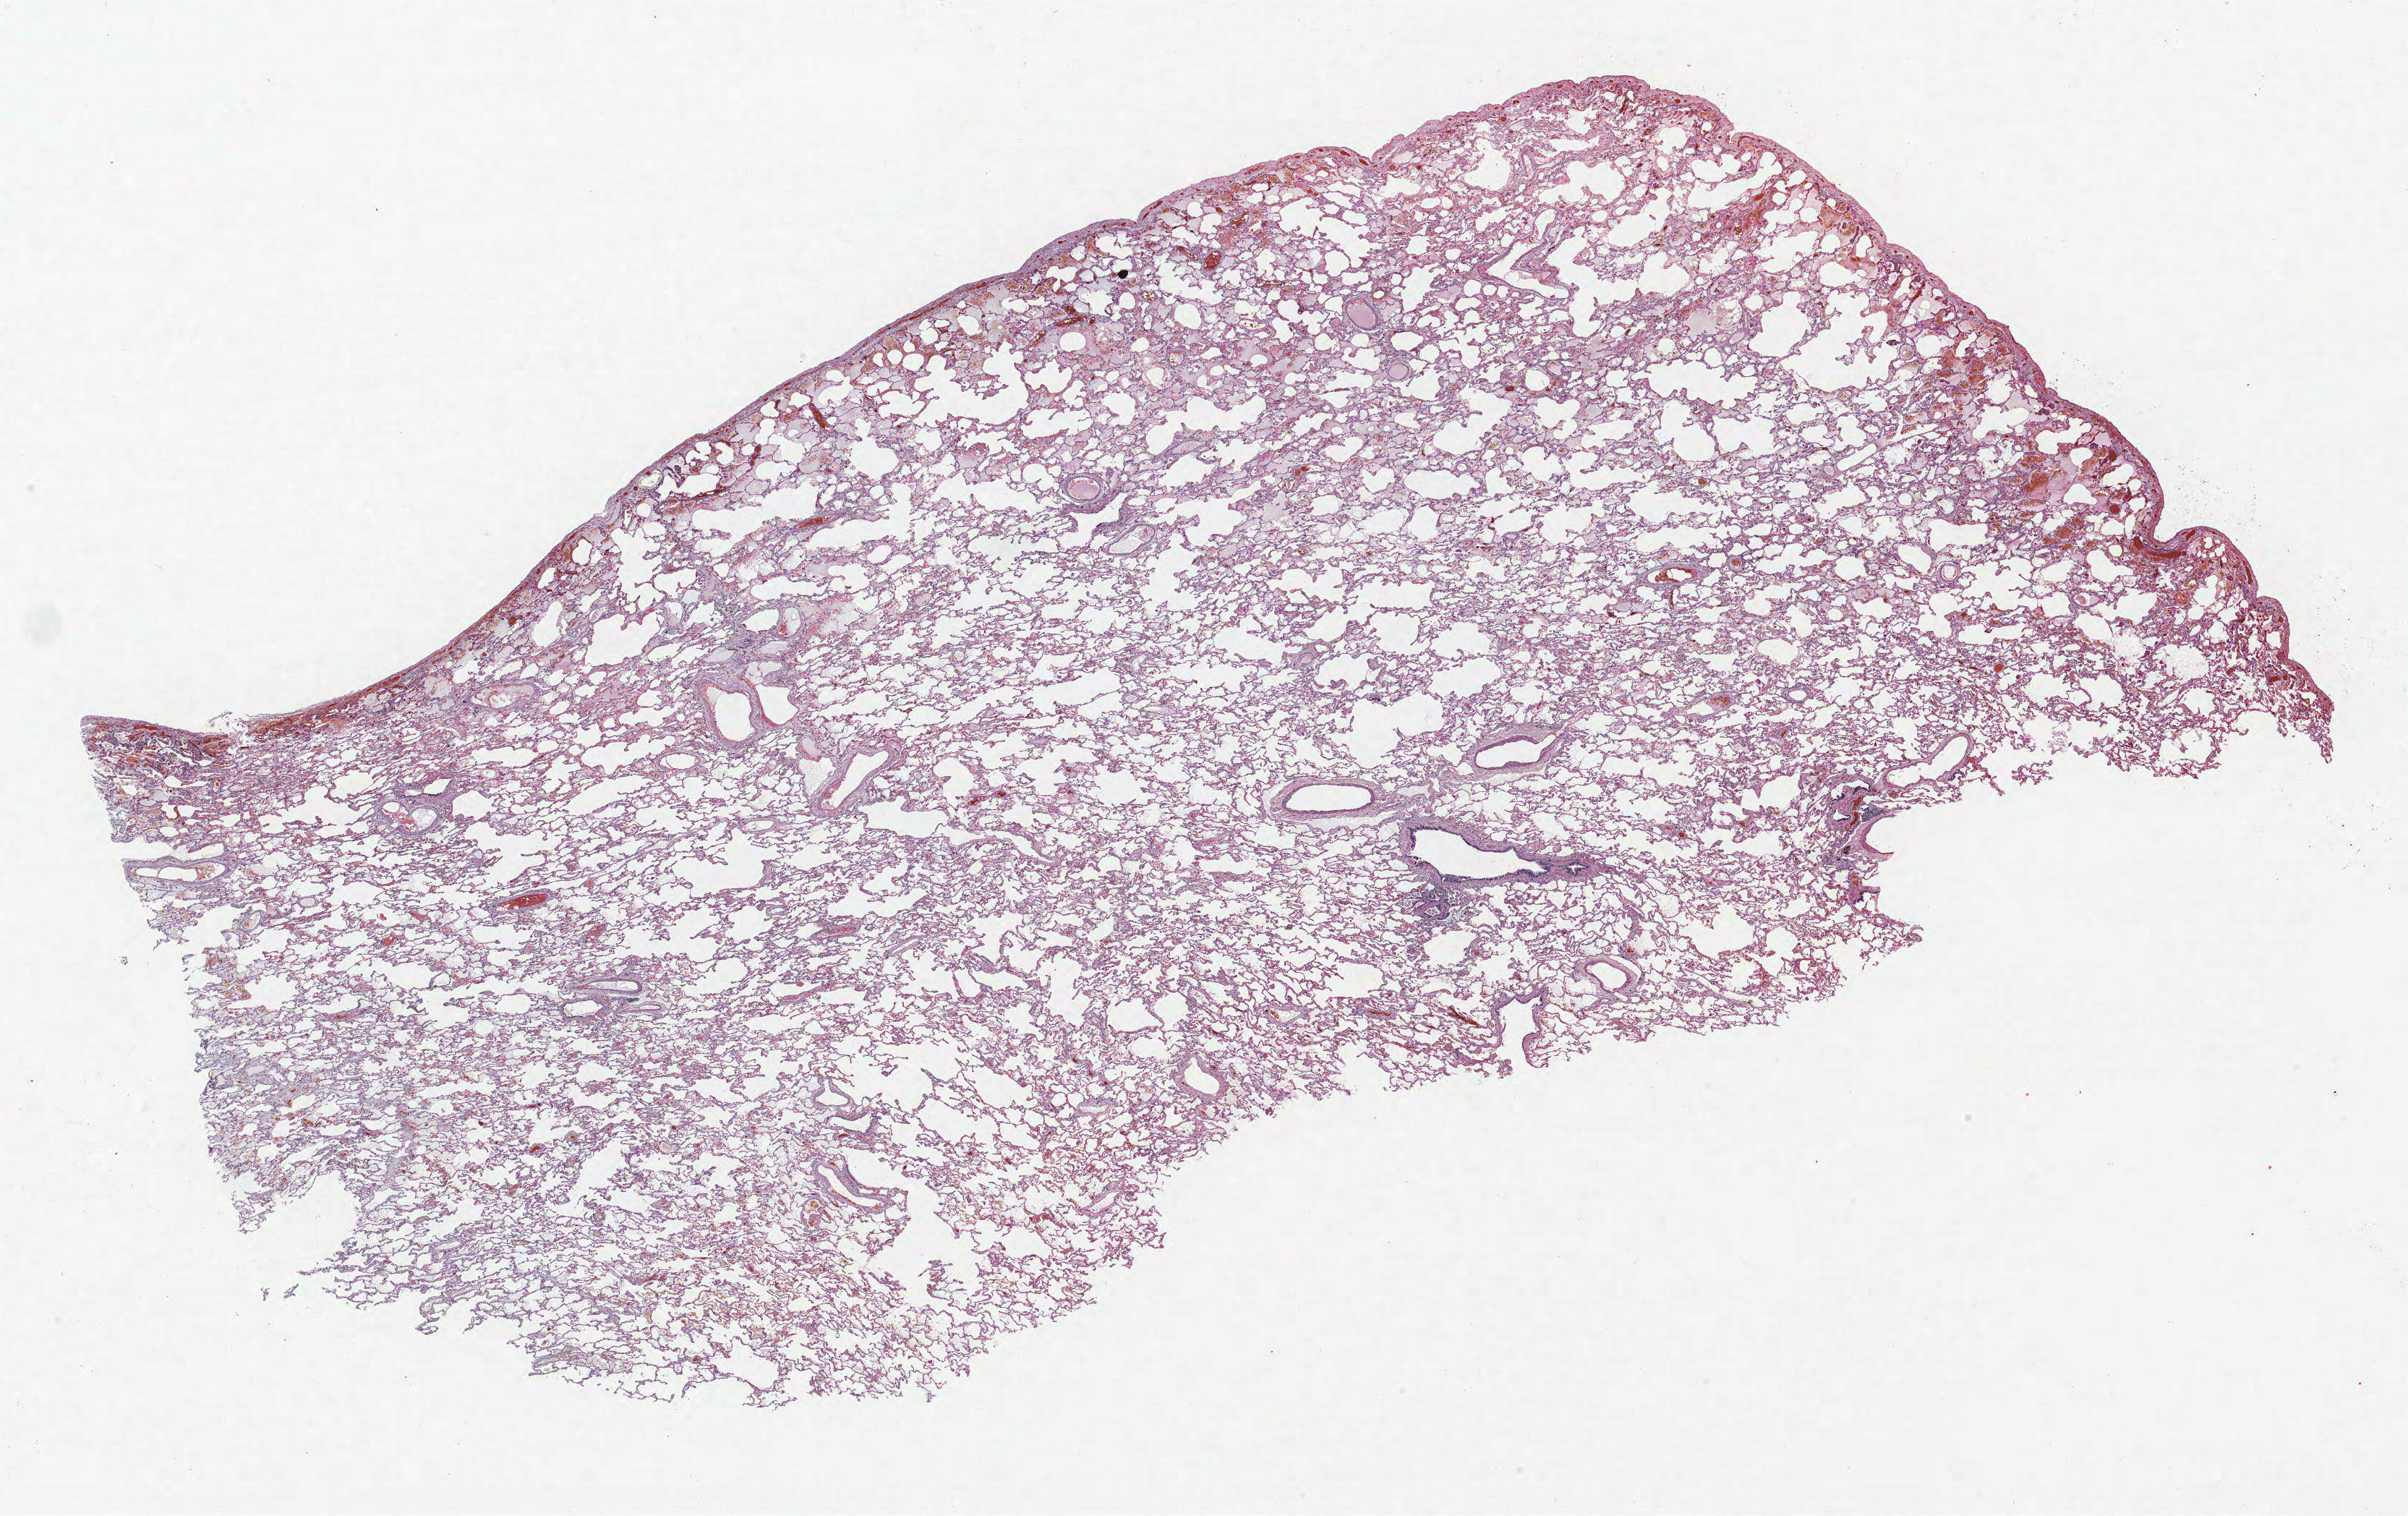
H&E-stained whole-slide image — whole scanned area (about 26.6 x 16.8 mm, from a 40x scan) shown as a low-resolution overview; FFPE section; lung. Female patient, aged 56 at enrolment. Former smoker at enrolment. Grade: poorly differentiated (G3).
• stage (AJCC 6th edition): IA
• primary tumour location (clinical record): right upper lobe
• participant's lung-cancer diagnosis: Squamous cell carcinoma, NOS
• tumour size (pathology): 11 mm